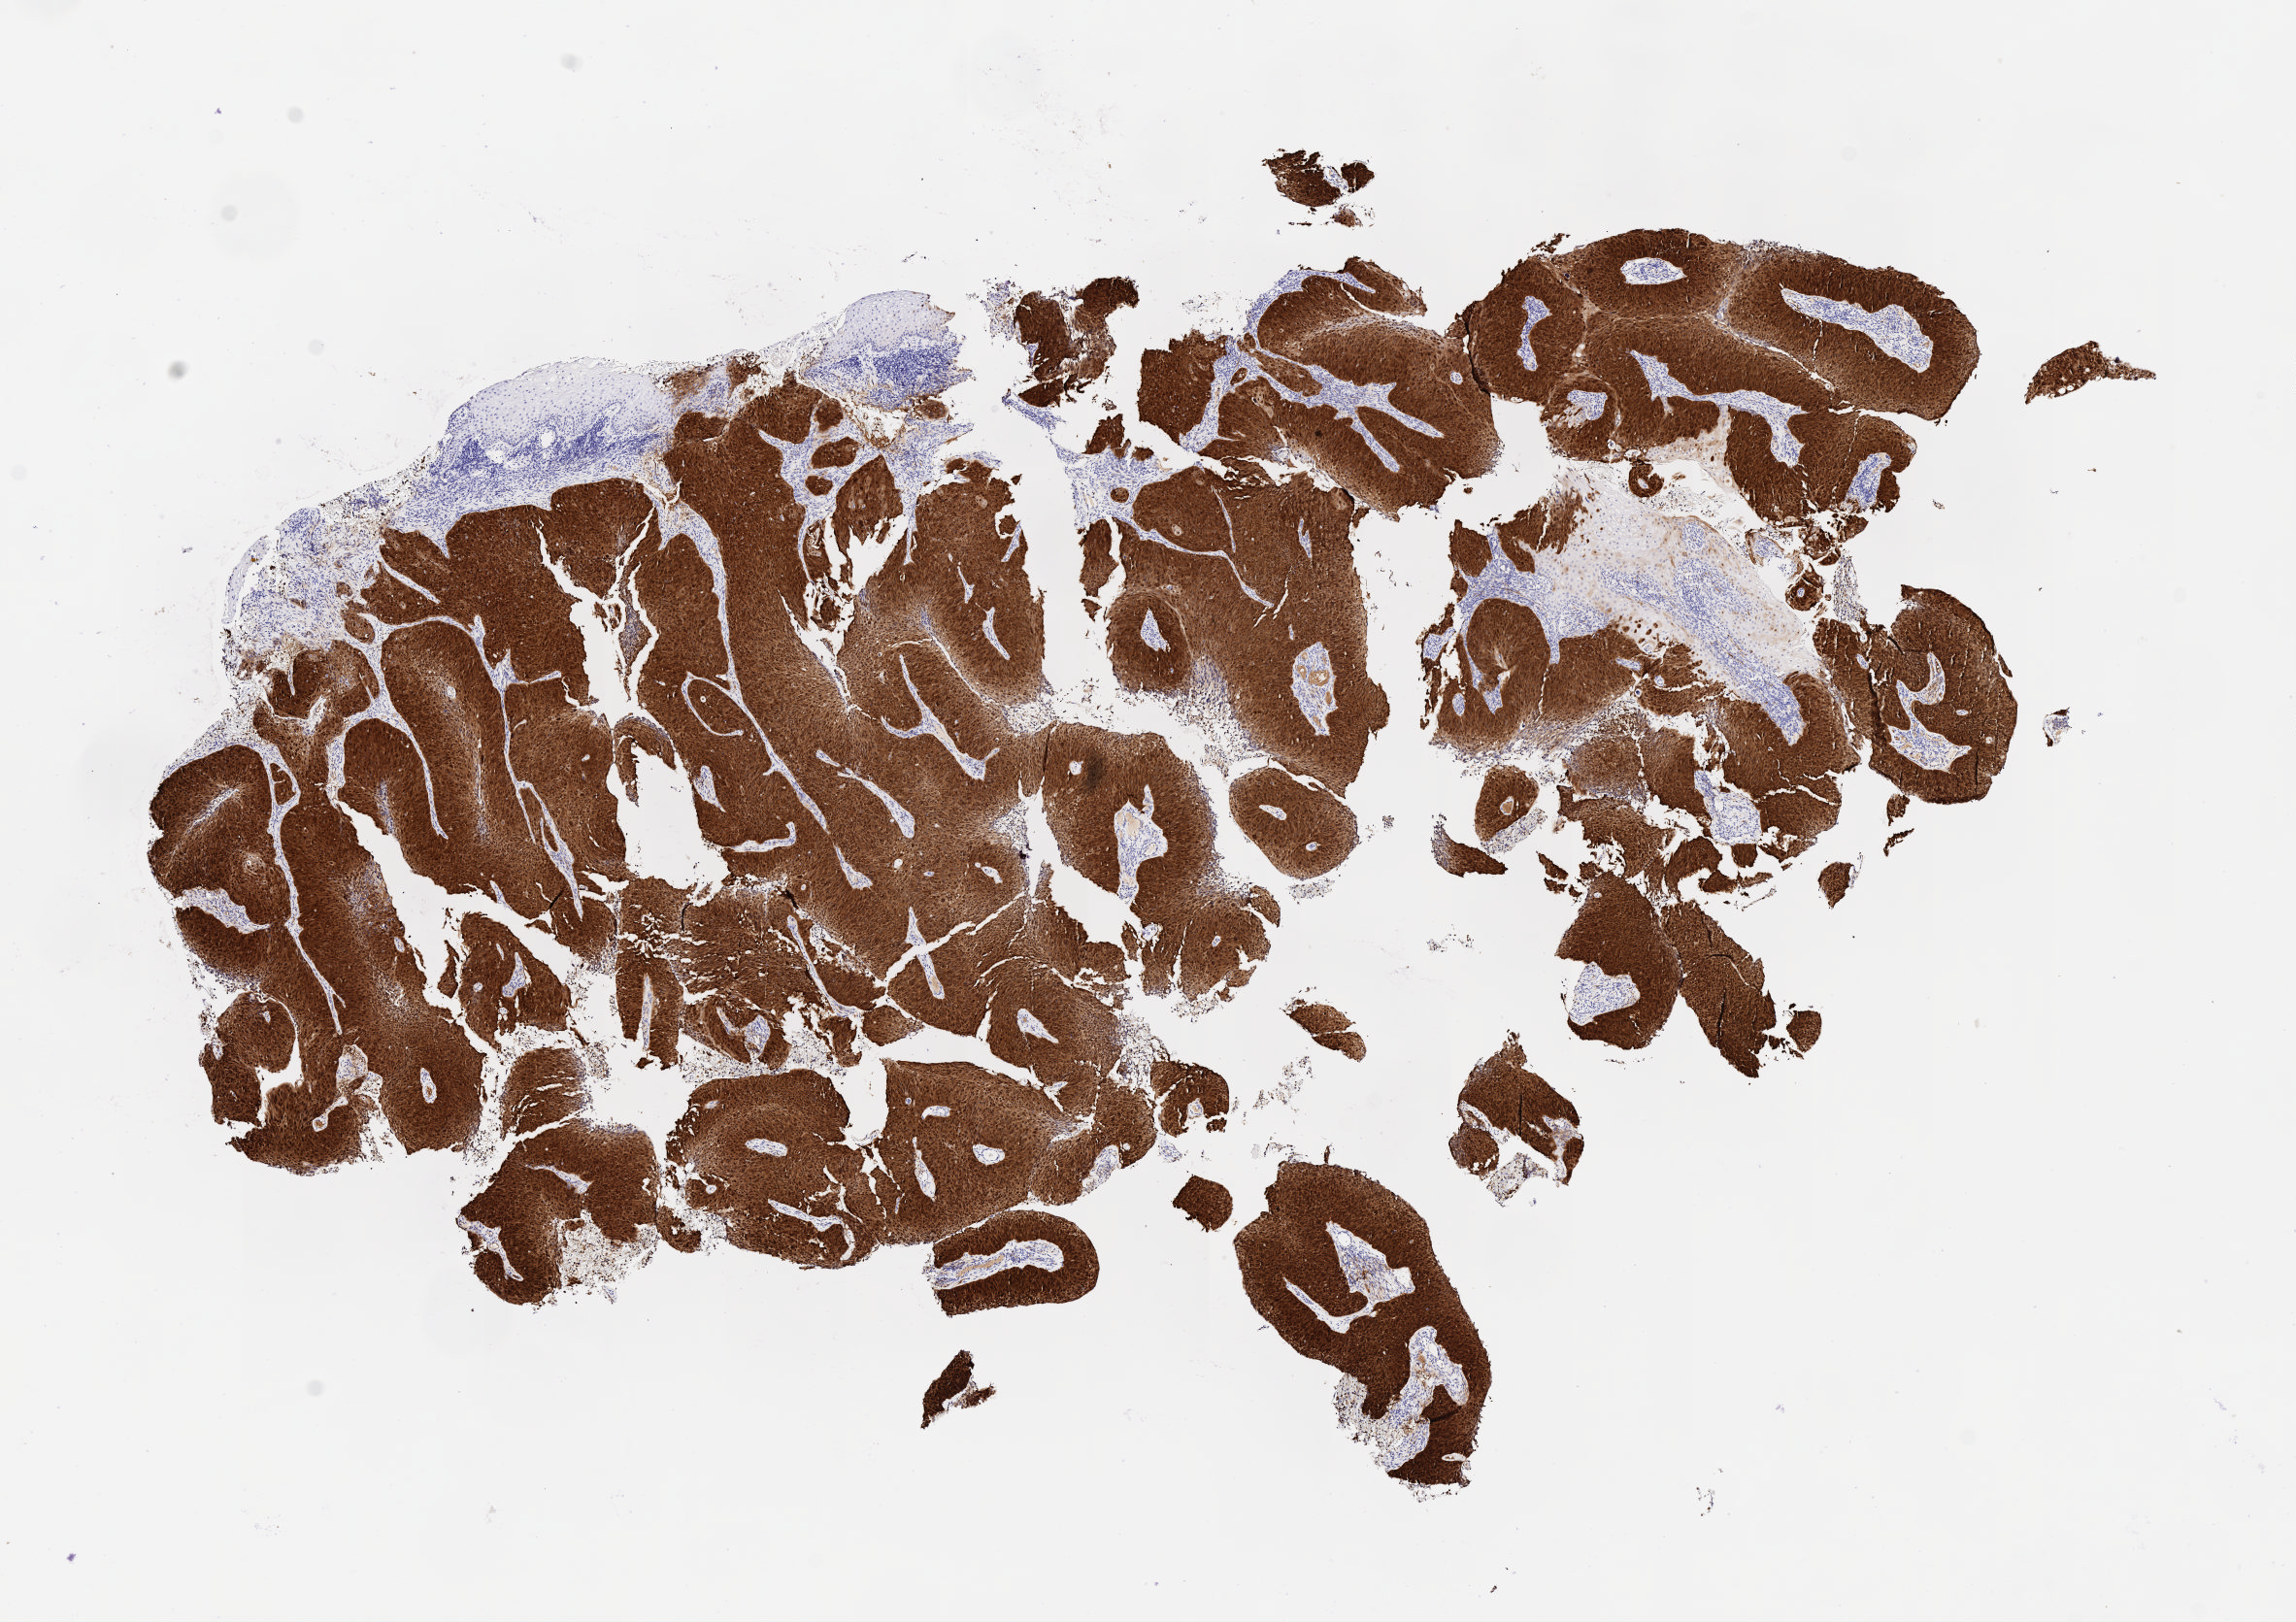
Whole-slide image, immunohistochemical stain for p16 (p16INK4a) — low-resolution overview of the scanned area, about 9.6 x 6.8 mm; tumor tissue; anatomic site: cervix. Female patient, 46 years old.
Histologic diagnosis: Basaloid squamous cell carcinoma.